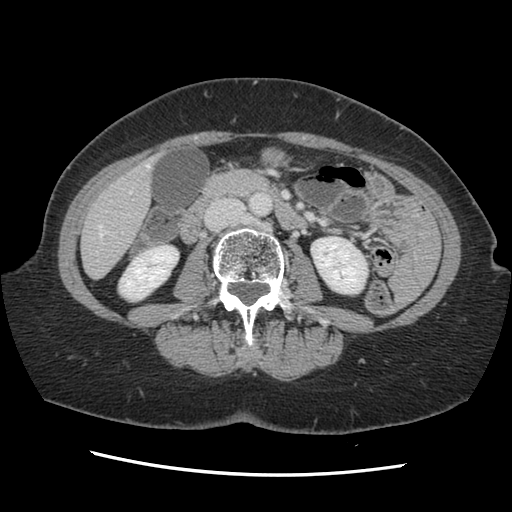
Contrast-enhanced abdominal CT, one axial slice; position 42 of 141 along the scan axis; soft-tissue window (W 400 / L 40 HU); 2.5 mm slice thickness; 512 × 512 image matrix, field of view 330 × 330 mm. Female patient, age 61 years. From the clinical record (not read from this slice): diagnosis: colorectal cancer liver metastases, imaged before liver resection; multiple liver metastases: no; largest metastasis: 2.4 cm; chemotherapy before resection: no.
Outlined on this slice (outlined manually by an expert reader):
- hepatic veins: box from (x=96, y=163) to (x=150, y=274) px
- liver: (x=82, y=164)–(x=153, y=277)
- planned liver remnant (the part of the liver to remain after resection): (x=83, y=171)–(x=152, y=277)